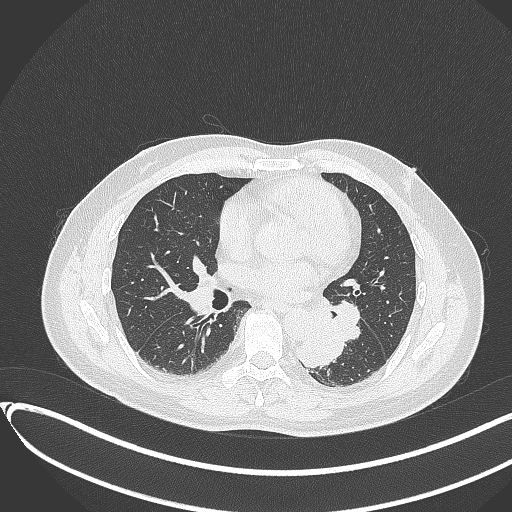
Chest CT, one axial slice; slice 168 of 417 in the series (ordered by position); reconstruction kernel B70f; 120 kVp; lung window (W 1500 / L -600 HU); 512 × 512 image matrix, field of view 400 × 400 mm. Patient: male, 54 years. Case-level facts recorded for this patient, not image findings: clinical TNM (as recorded): T3 N0 M0.
Annotated regions visible in this slice (rectangle marked by the reading radiologist):
- lung tumour (recorded histology: squamous cell carcinoma): box from (x=296, y=326) to (x=351, y=371) px